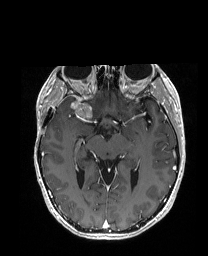
Brain MRI from a brain-tumour surgery series, one axial slice. Slice 104 of 192 in the series (ordered by position). T1-weighted post-contrast. 1 mm slice thickness. 208 × 256 image matrix, field of view 203 × 250 mm. Case-level facts recorded for this patient, not image findings: histopathology: Metastatic Carcinoma from Breast primary; tumour location: Right Frontal.
Structures marked on this image (manually delineated by an expert):
- tumour: bounding box <55,98,104,118> (left, top, right, bottom; pixels)